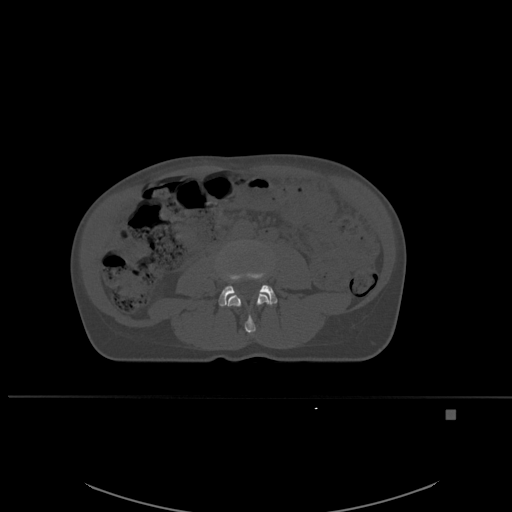
CT including the spine, one axial slice. Slice 202 of 537 in the series (ordered by position). Bone window (W 1800 / L 400 HU). 1.5 mm slice thickness. 512 × 512 image matrix, field of view 440 × 440 mm. Female patient, age 45 years. Case-level facts recorded for this patient, not image findings: primary cancer: lung.
Structures marked on this image (semi-automatic segmentation, software-assisted and operator-edited):
- L3 vertebra: box from (x=227, y=292) to (x=270, y=333) px
- L4 vertebra: (x=218, y=272)–(x=277, y=306)